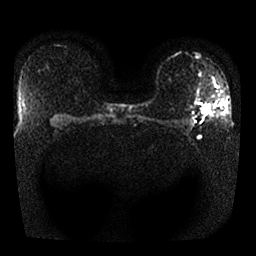
Breast MRI, one axial slice; position 19 of 25 along the scan axis; diffusion-weighted series; image 2 of 4 stored at this slice position (different b-values; order by instance number); 1.5 T; 4 mm slice thickness; 256 × 256 image matrix. Female patient.
Structures marked on this image (outlined manually by an expert reader):
- tumour on diffusion-weighted imaging: box from (x=202, y=105) to (x=210, y=113) px